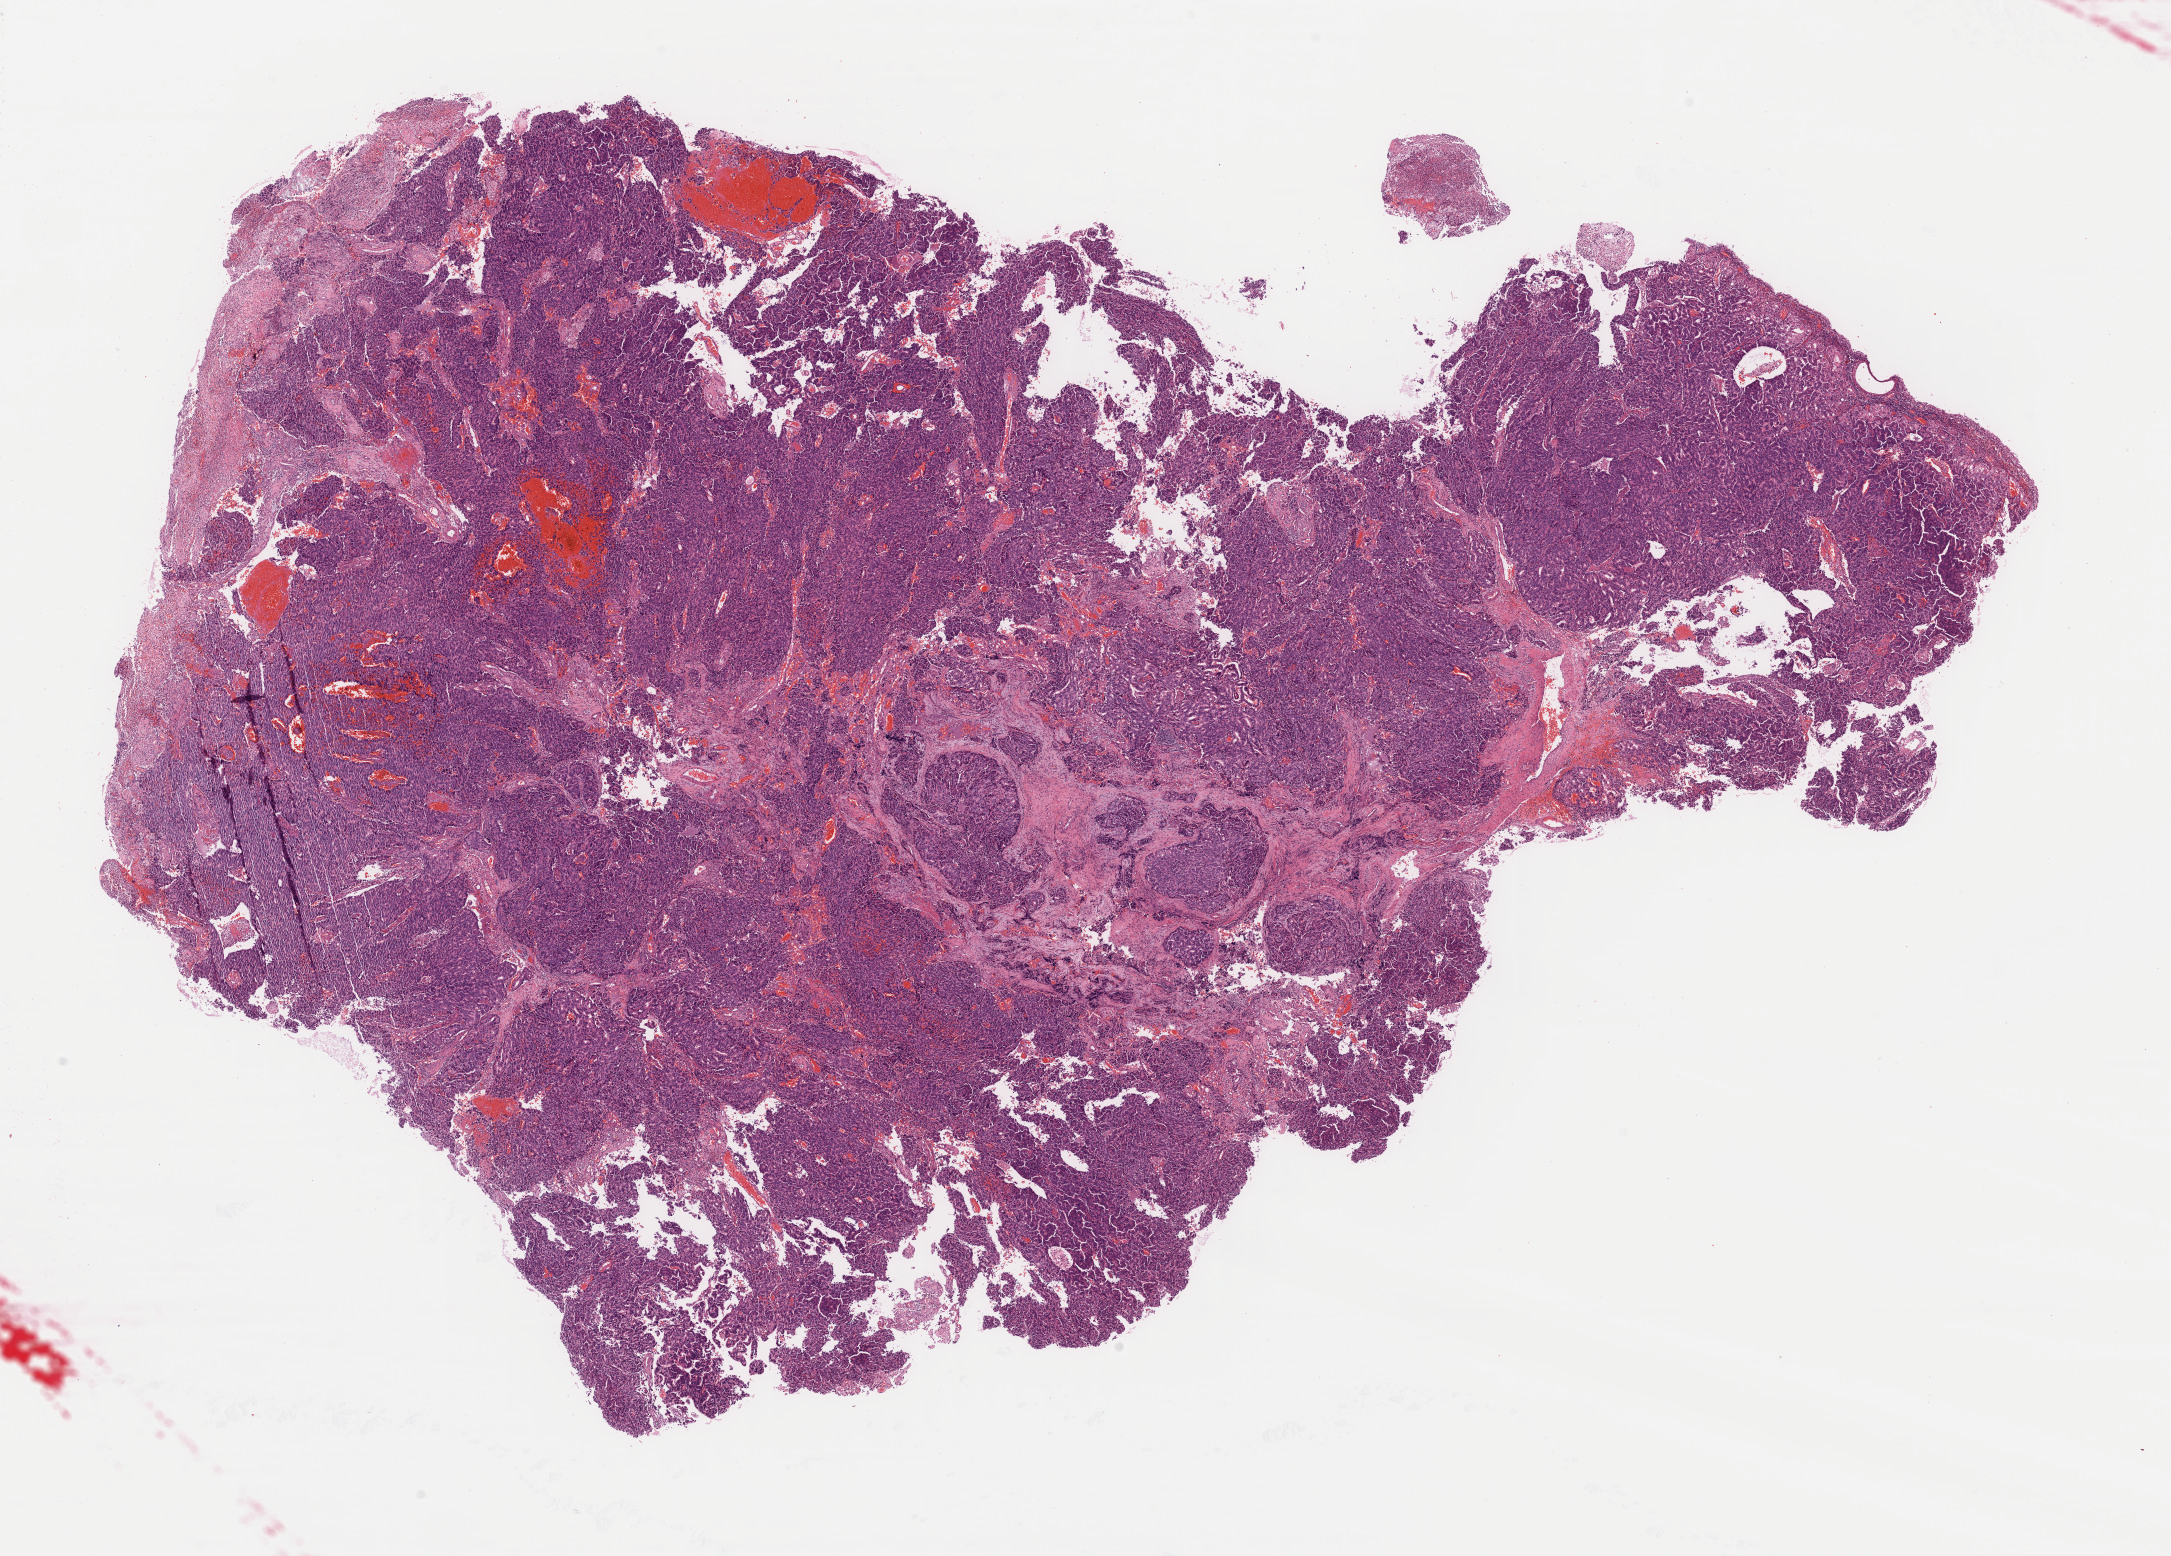
Digitized Hematoxylin and eosin (H&E) stained tissue section (whole slide), low-resolution overview of the scanned area, about 17.2 x 12.3 mm; formalin-fixed paraffin-embedded (FFPE) diagnostic section; primary tumour sample from the prostate. Male, age 70 years at initial diagnosis. Gleason score: 8 (5+3).
- laterality: bilateral
- diagnosis: Adenocarcinoma, NOS (prostate gland)